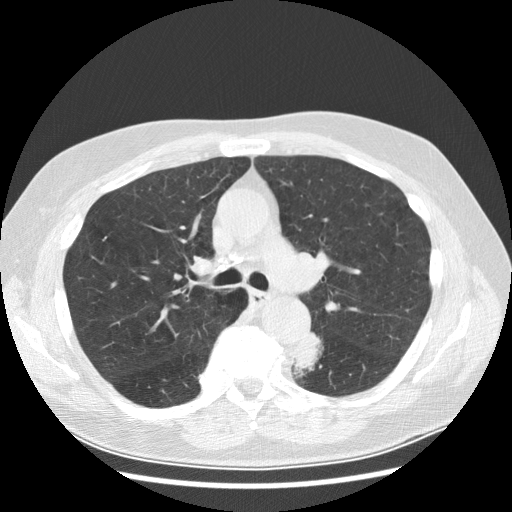
Low-dose screening chest CT, axial slice; first (baseline) screen; lung window (W 1500 / L -600 HU); 120 kVp; slice 98 of 282 in the series. Male, age 70 years at enrolment. Current smoker at enrolment.
• Expert-annotated lung lesion, bounding box (x1, y1, x2, y2) in pixels: (277, 334, 326, 380).
• Reader record for this screening exam (exam-level; its link to the box is not recorded): non-calcified nodule or mass ≥4 mm, left lower lobe, 27 × 16 mm, spiculated (stellate) margins, soft tissue attenuation, pre-existing on the prior screen: yes; interval growth: yes.
• Lung cancer was diagnosed 97 days after this screen: papillary adenocarcinoma, NOS, left lower lobe, moderately differentiated (G2), stage IB (AJCC 6th edition), 35 mm at pathology.